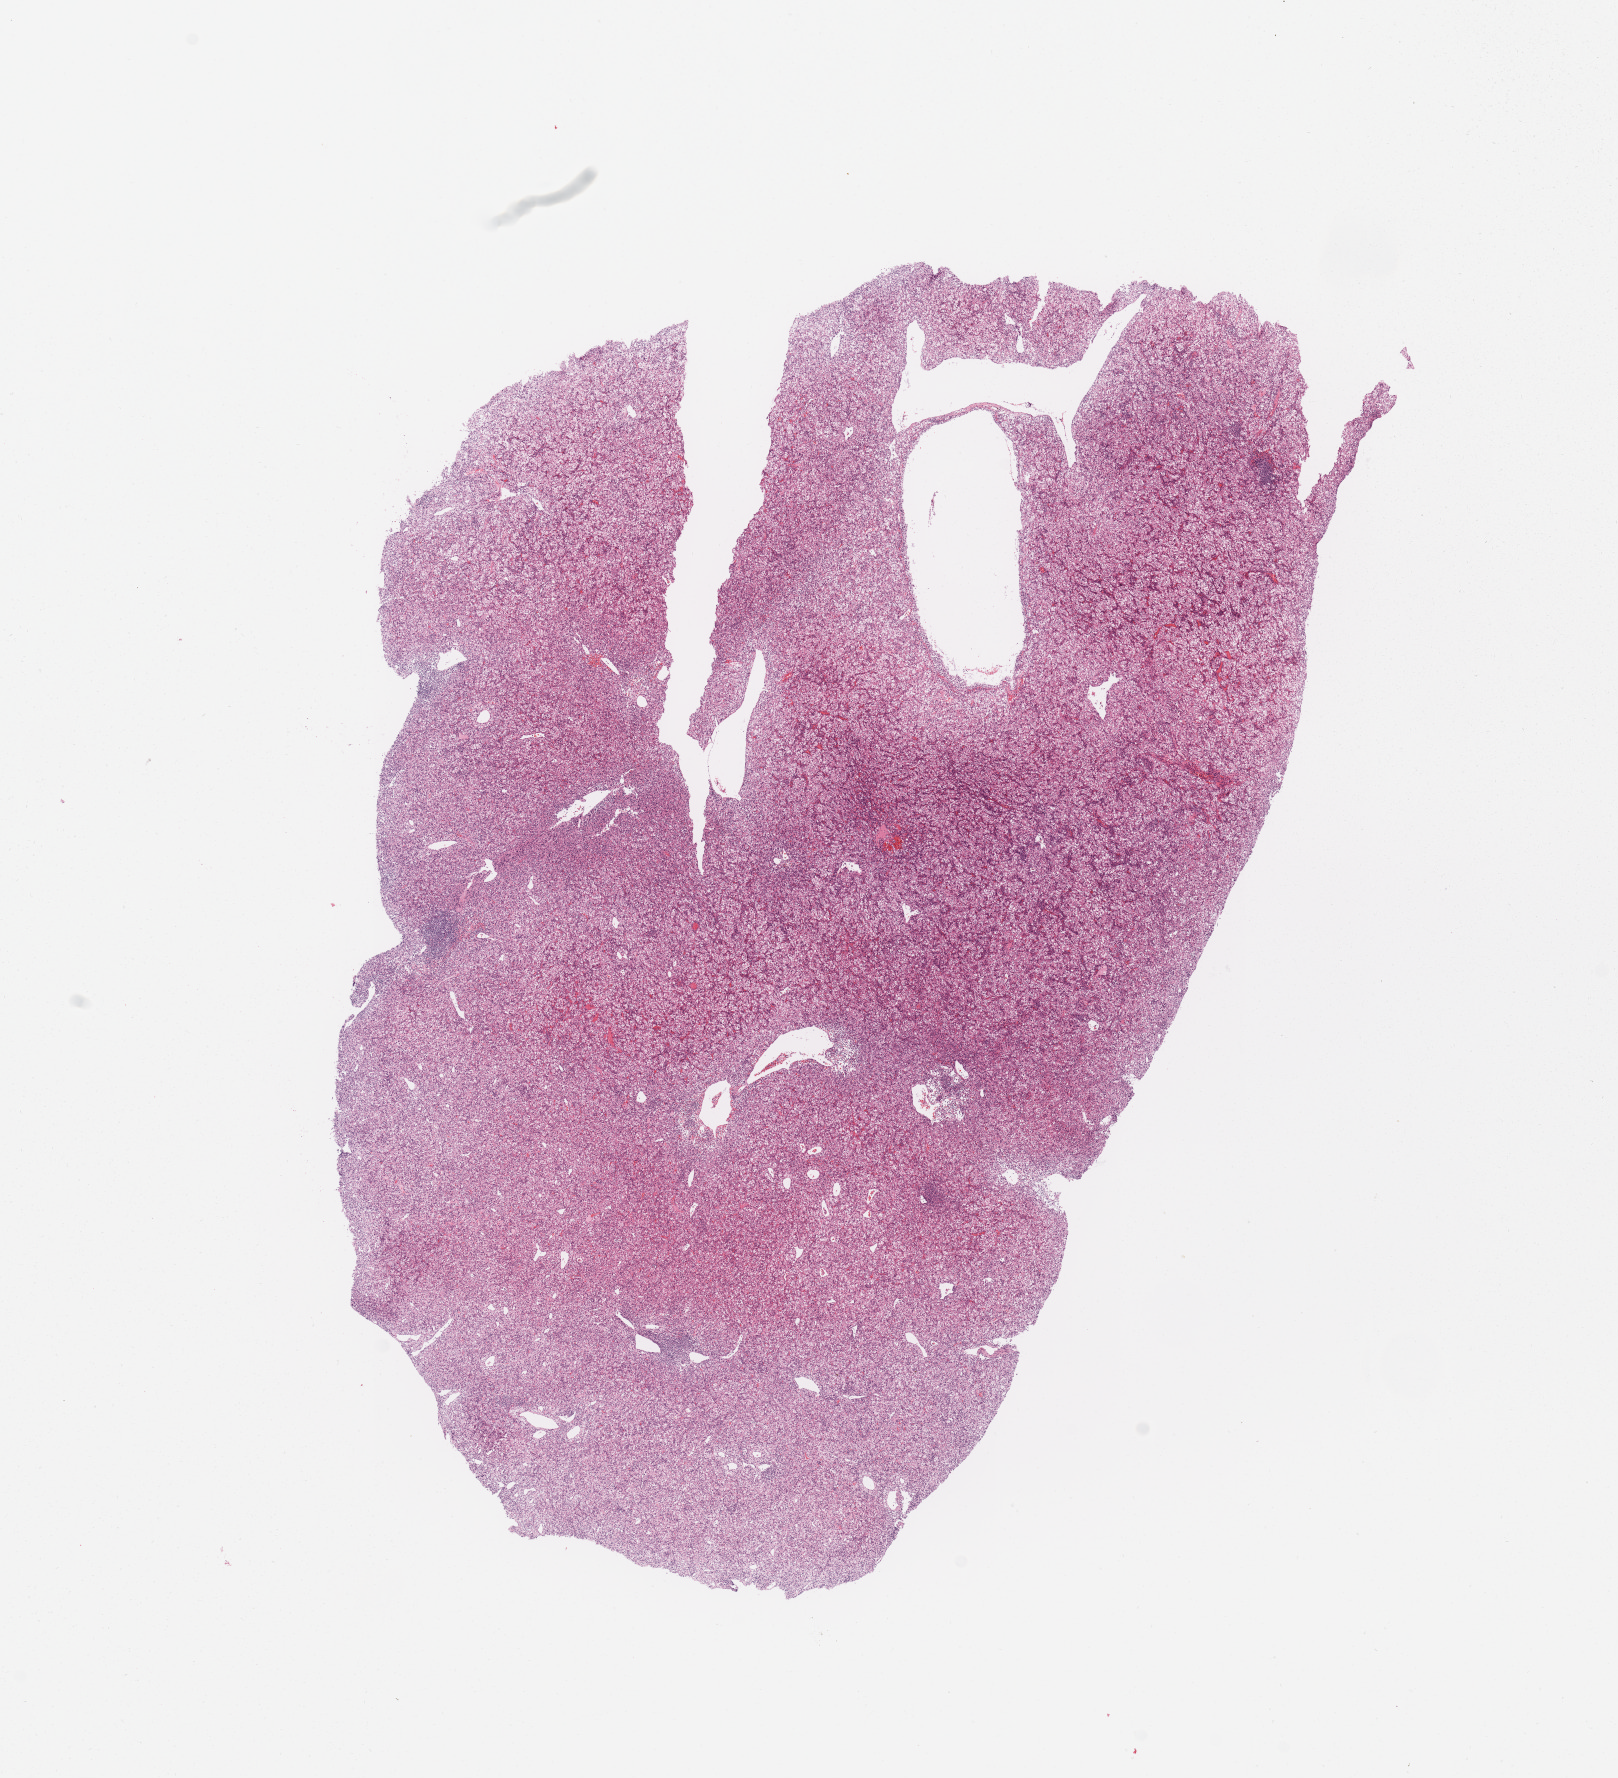
Whole-slide histology image, Hematoxylin and eosin (H&E) stained — whole scanned area (about 12.8 x 14.1 mm, acquisition: 20x scan) shown as a low-resolution overview; tumour tissue sample, sampled site: kidney. Male, 47 y/o. Histologic grade: G2 (moderately differentiated). Composition of this section per pathologist review: tumour nuclei 85%, necrosis 0%.
* histologic diagnosis: Renal cell carcinoma, NOS
* primary tumour site (as recorded): upper pole
* AJCC pathologic stage: I